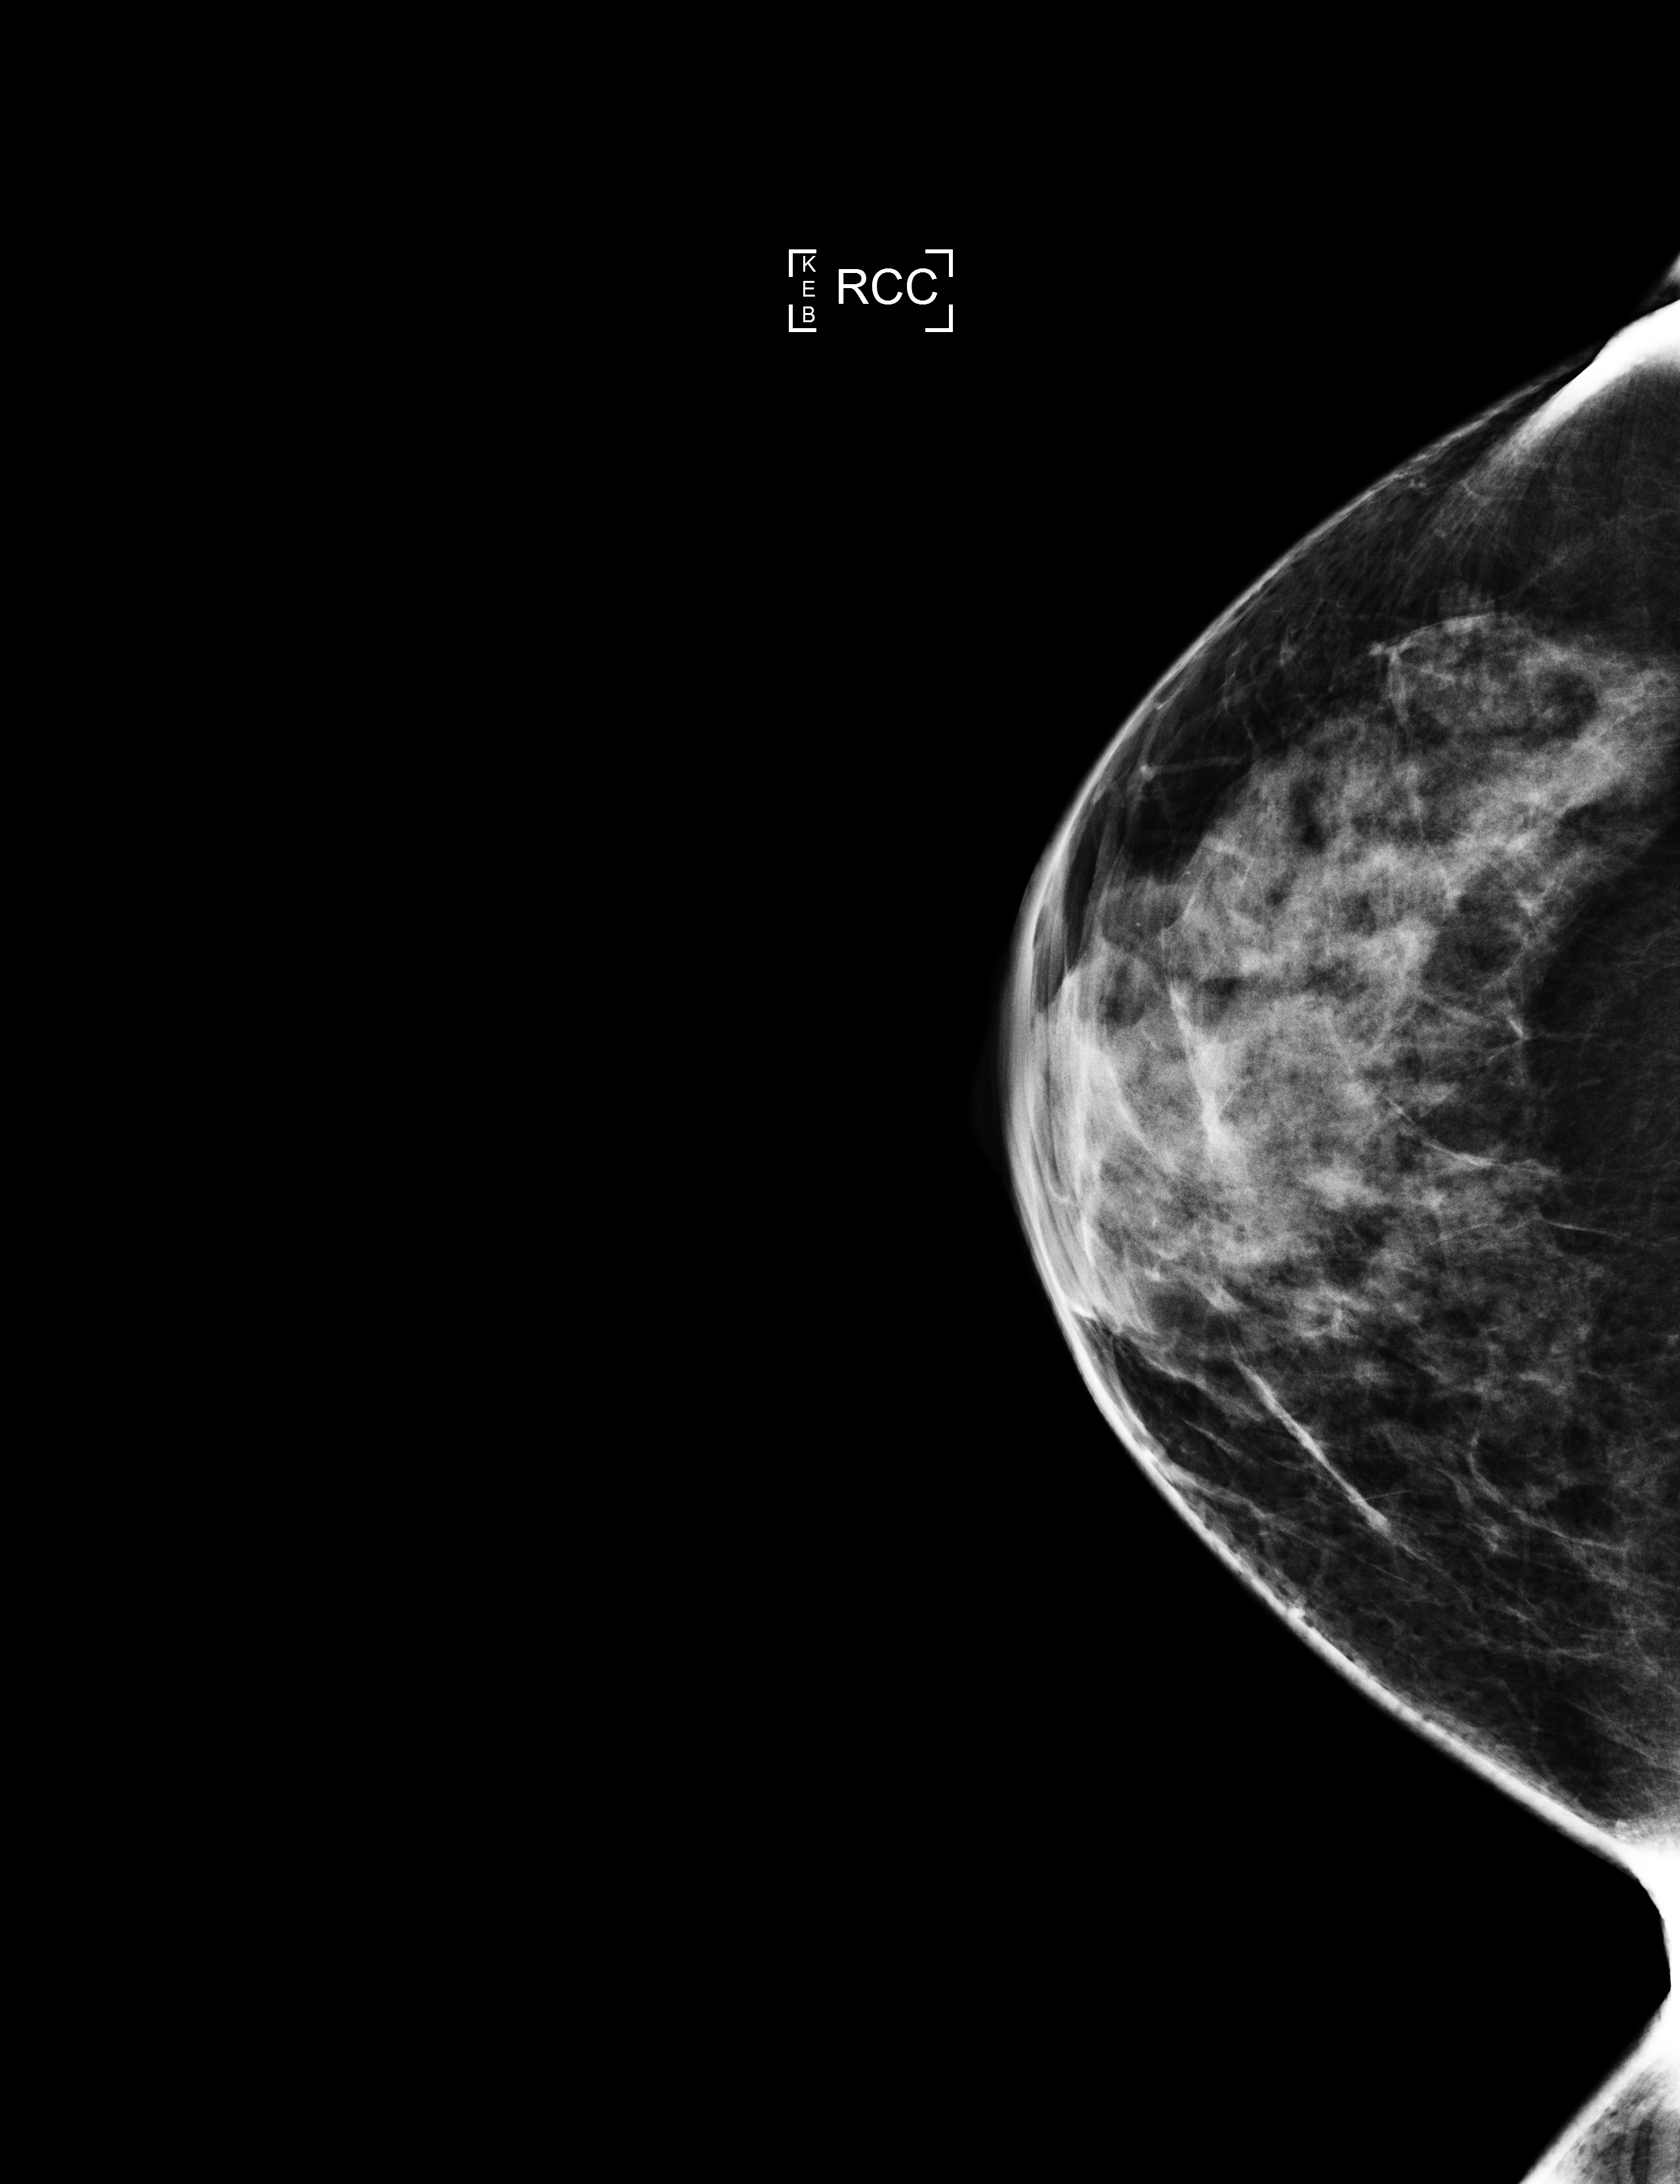
Full-field digital mammogram (FFDM); right breast; CC view; screening examination; compressed breast thickness 53 mm. Patient: female, 44 years.
- BI-RADS breast density category at the screening exam (both breasts, scale 1–4): 3
- final BI-RADS assessment for this screening round (tomosynthesis exam, both breasts): category 2
- recall: no recall after this screen